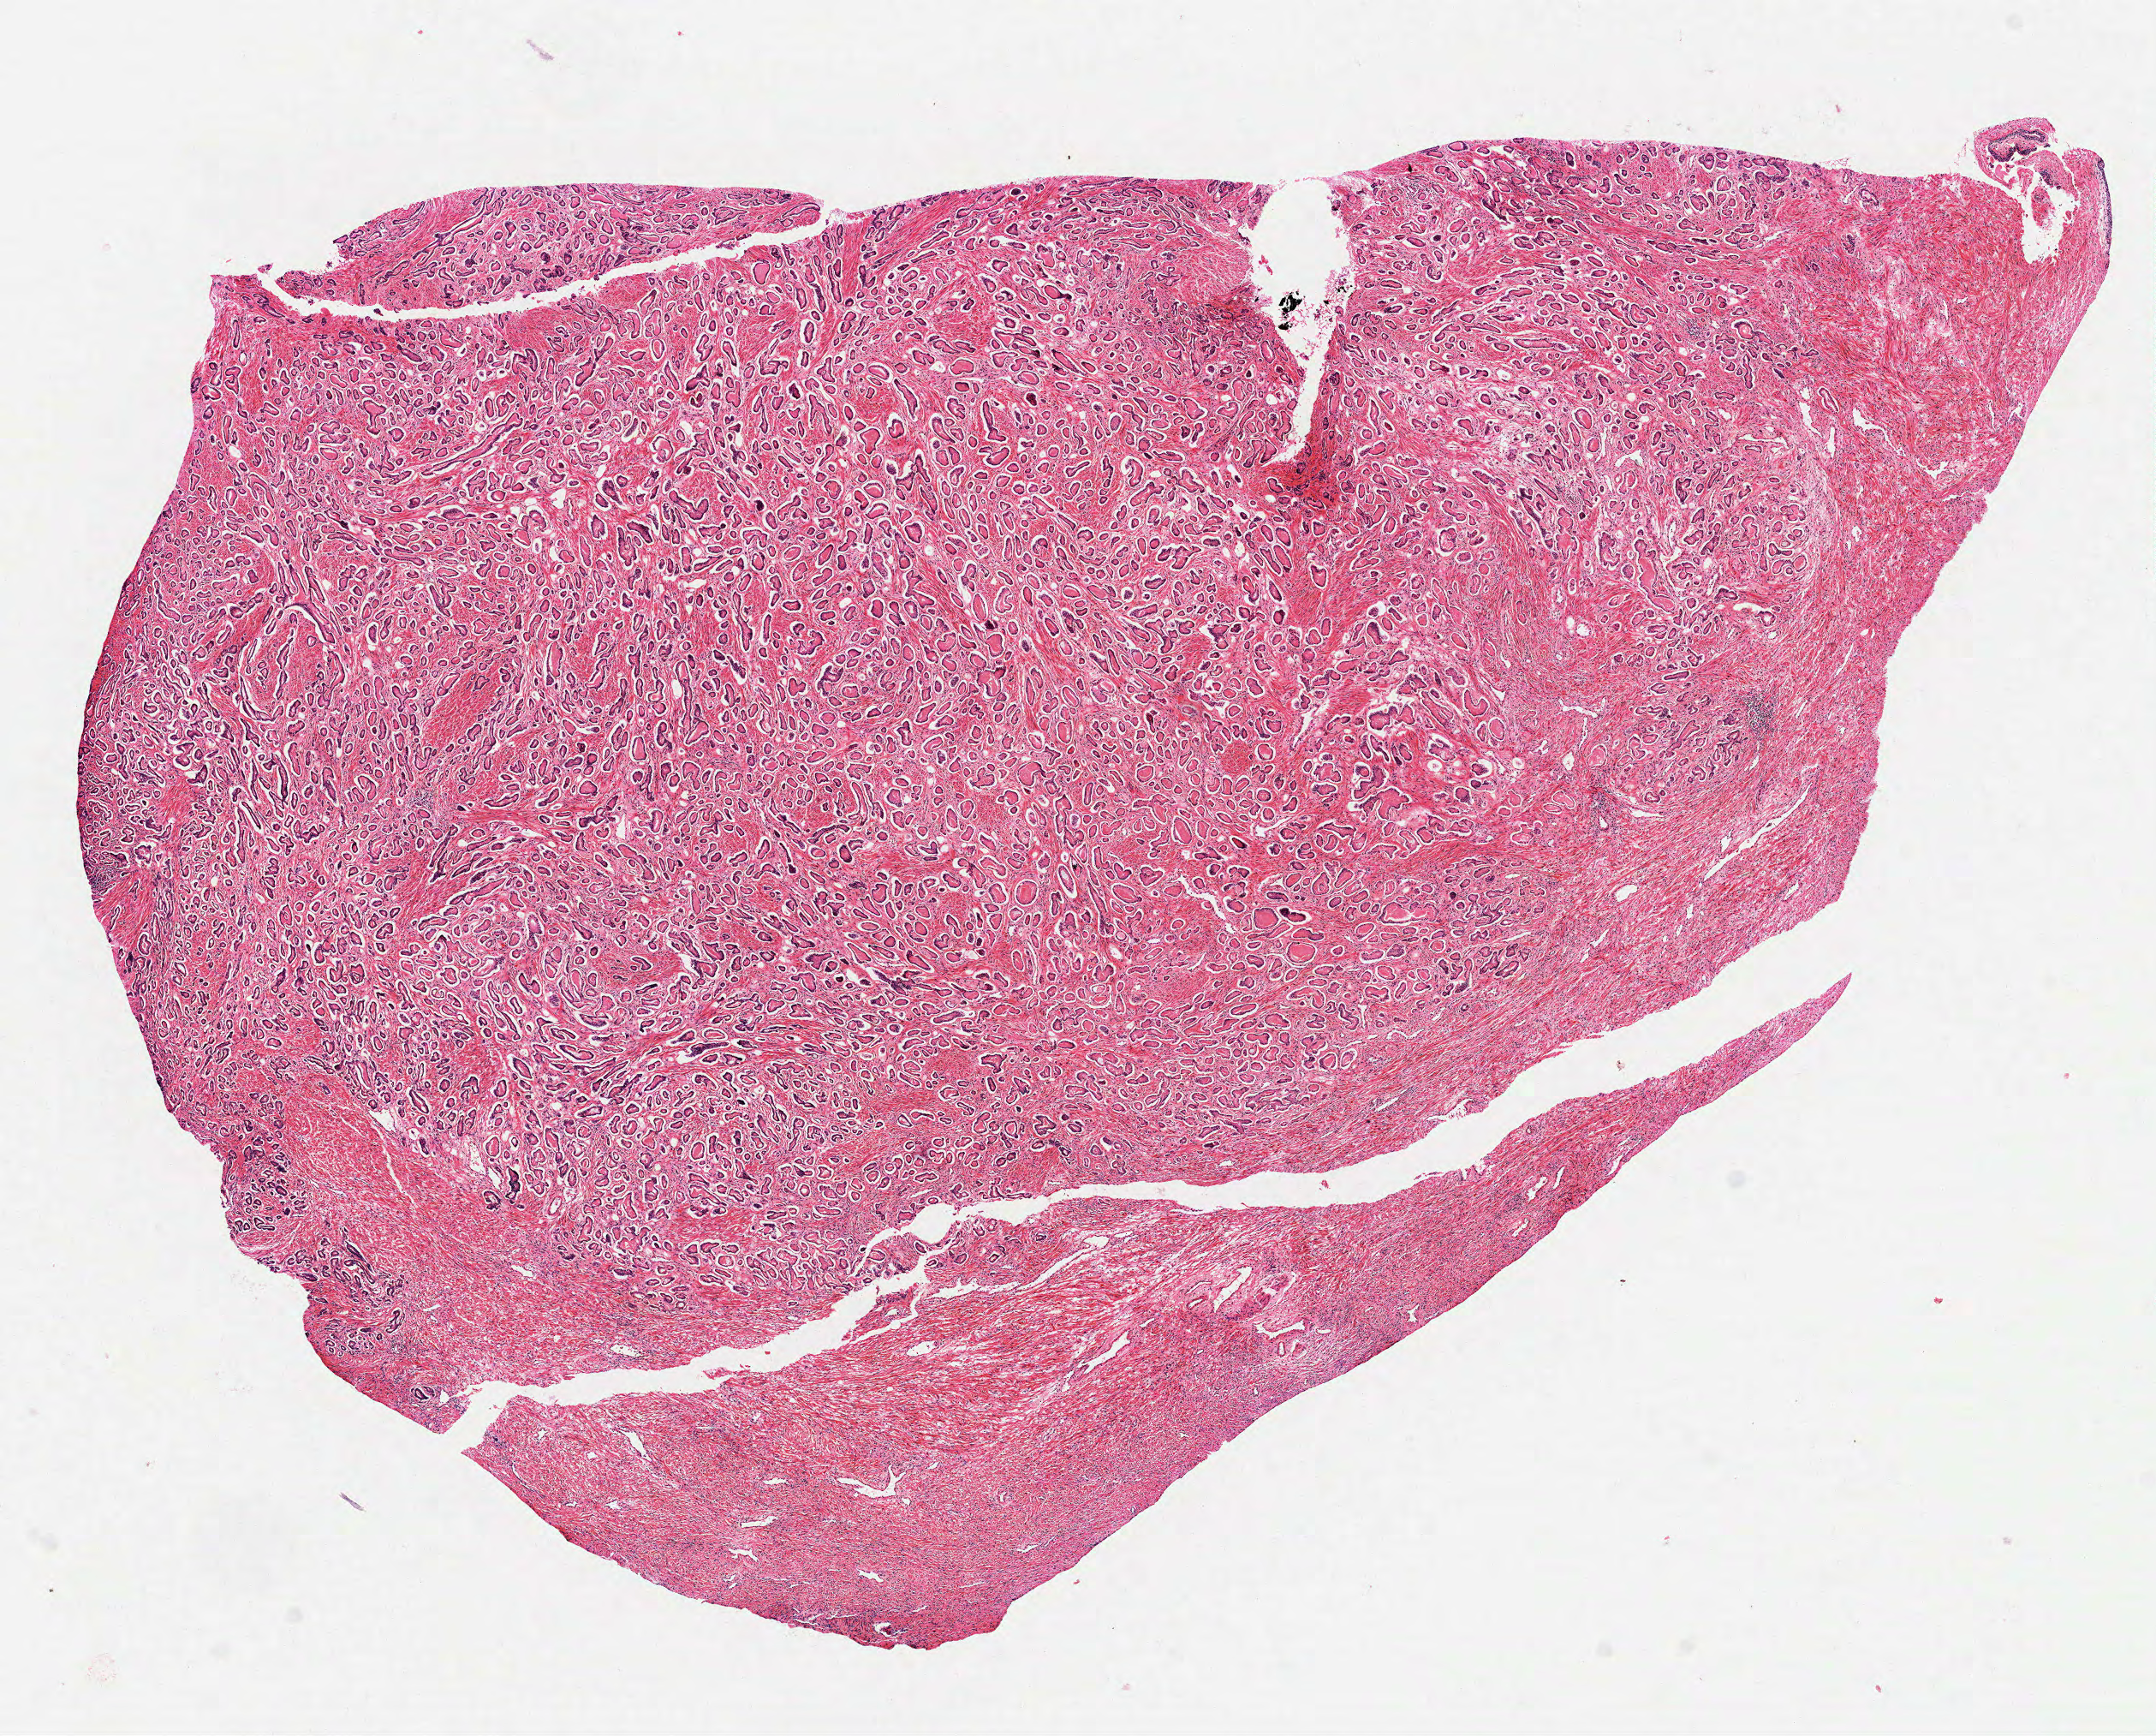
Digitized H&E tissue section (whole slide) — a low-resolution overview of the entire scanned area, about 10.2 x 8.2 mm. Formalin-fixed paraffin-embedded (FFPE) diagnostic section. Primary tumour sample from the prostate. Patient: male, age at initial diagnosis 55 years. Gleason score: 7 (3+4).
Pathologic diagnosis: Acinar cell carcinoma (prostate gland). Lymph nodes positive (case pathology): 0 of 4 examined.